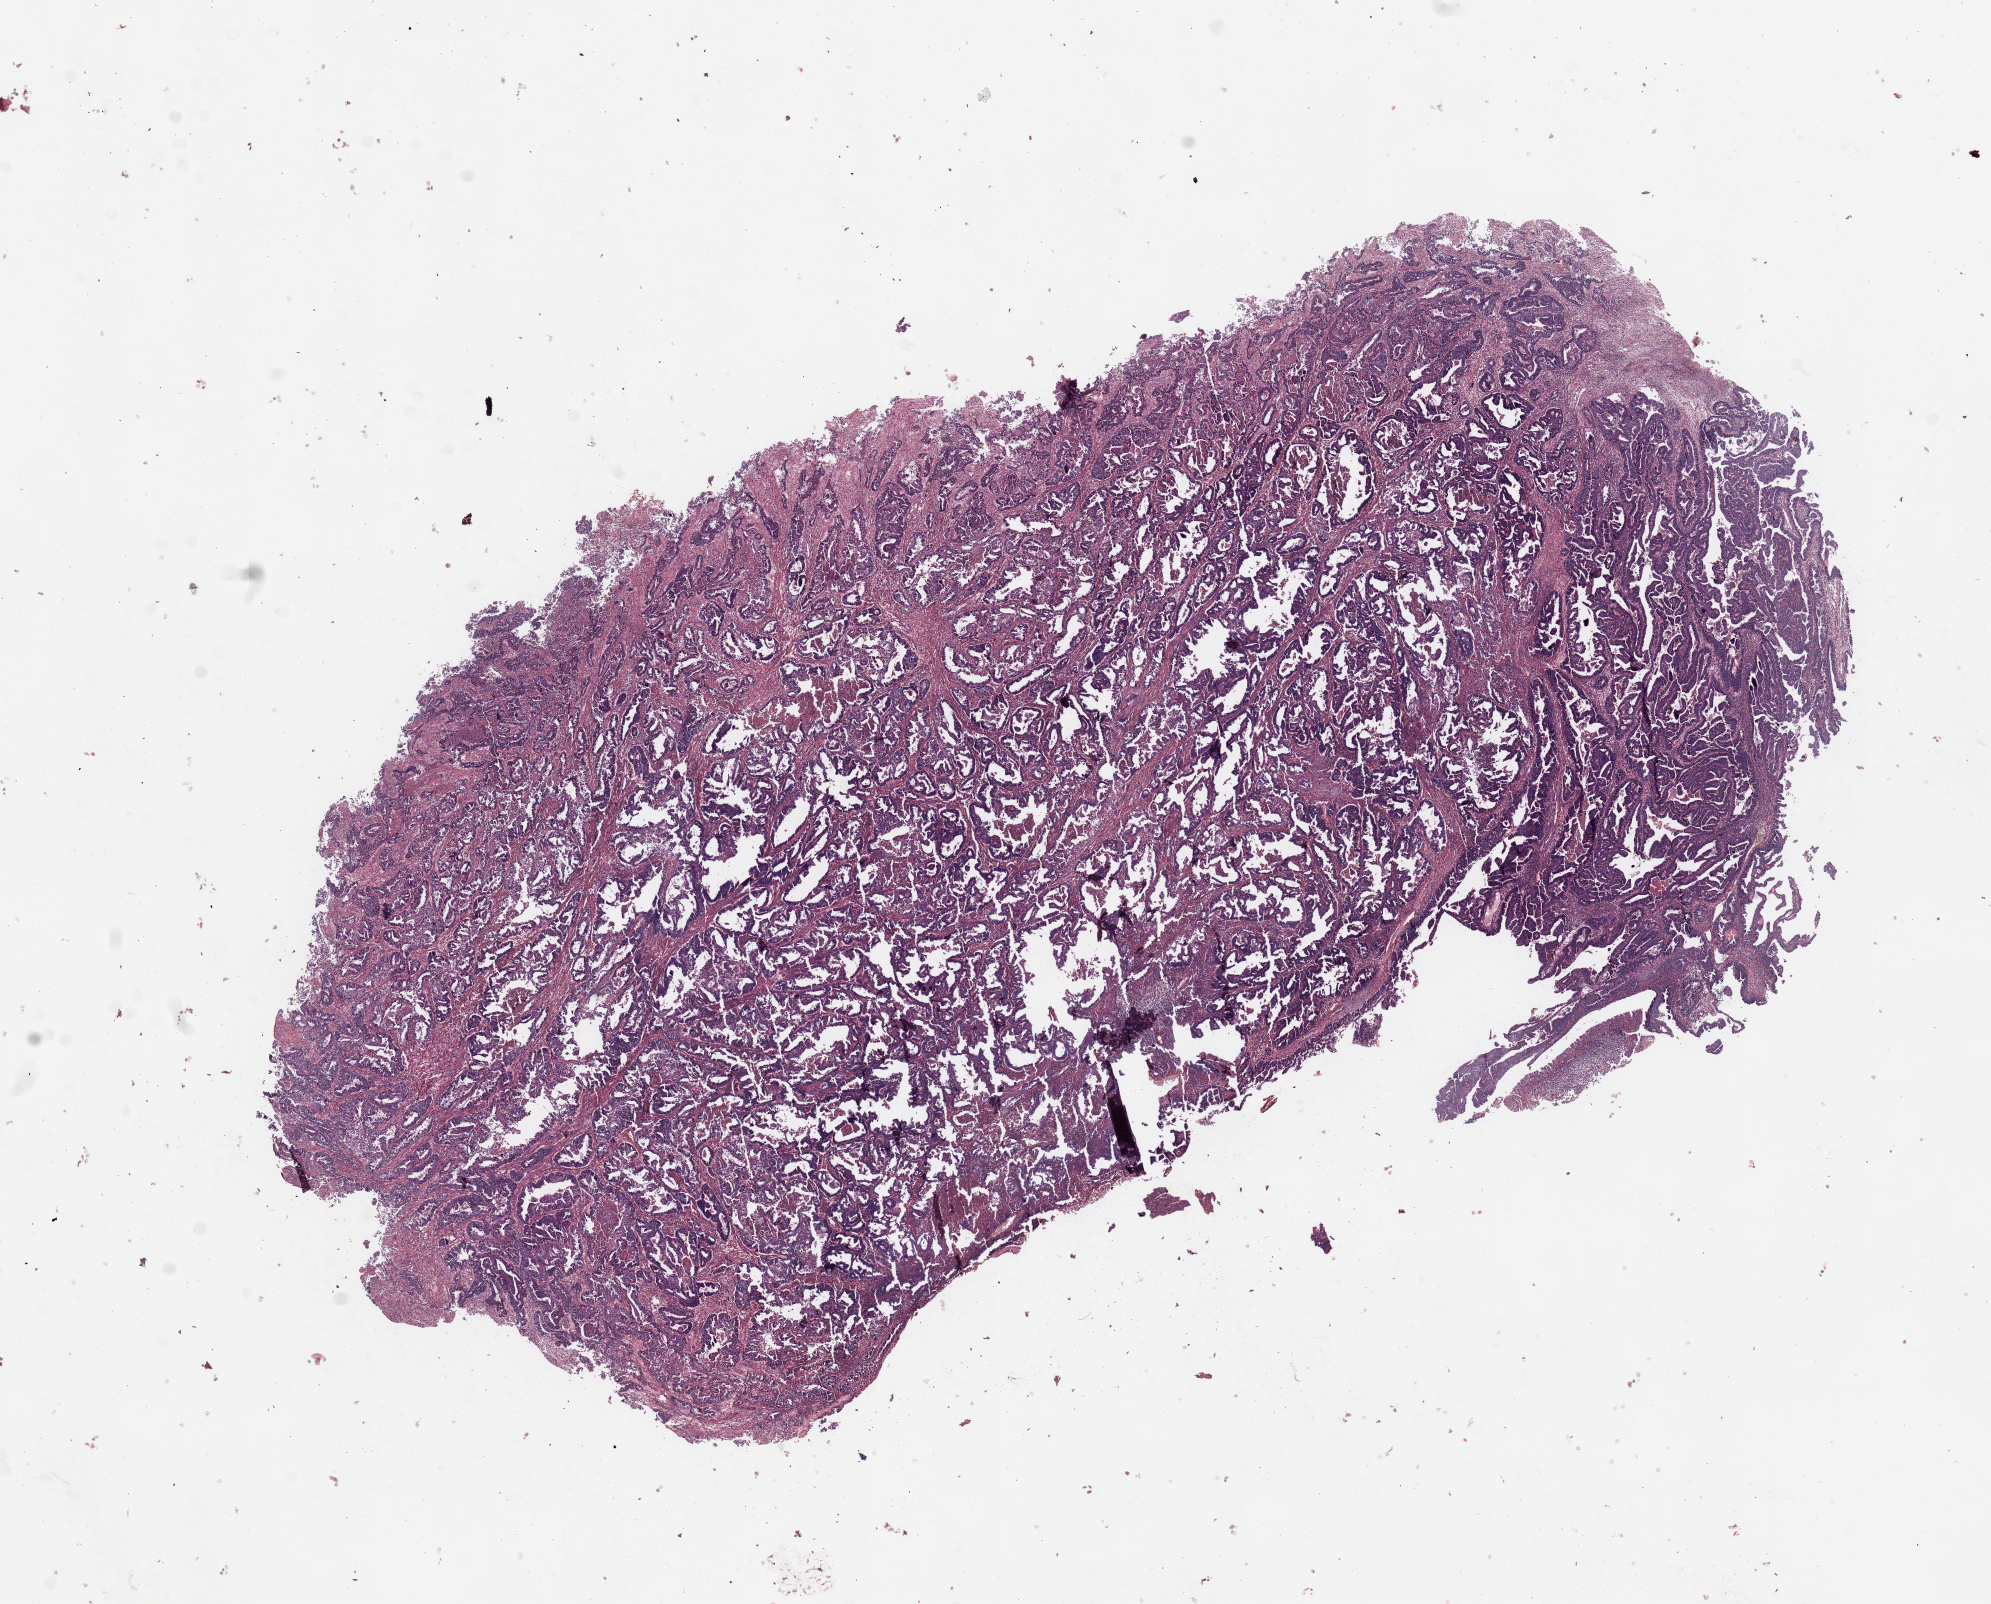
Digitized Hematoxylin and eosin (H&E) stained tissue section (whole slide), shown as a low-resolution overview of the whole scanned area (about 15.8 x 12.7 mm, acquisition: 20x scan); tumour tissue sample, sampled site: uterus. Female, 55 y/o. Histologic grade: G3 (poorly differentiated). Composition of this section per pathologist review: tumour nuclei 90%, necrosis 2%.
Diagnosis: Endometrioid adenocarcinoma, NOS. AJCC pathologic stage: I.